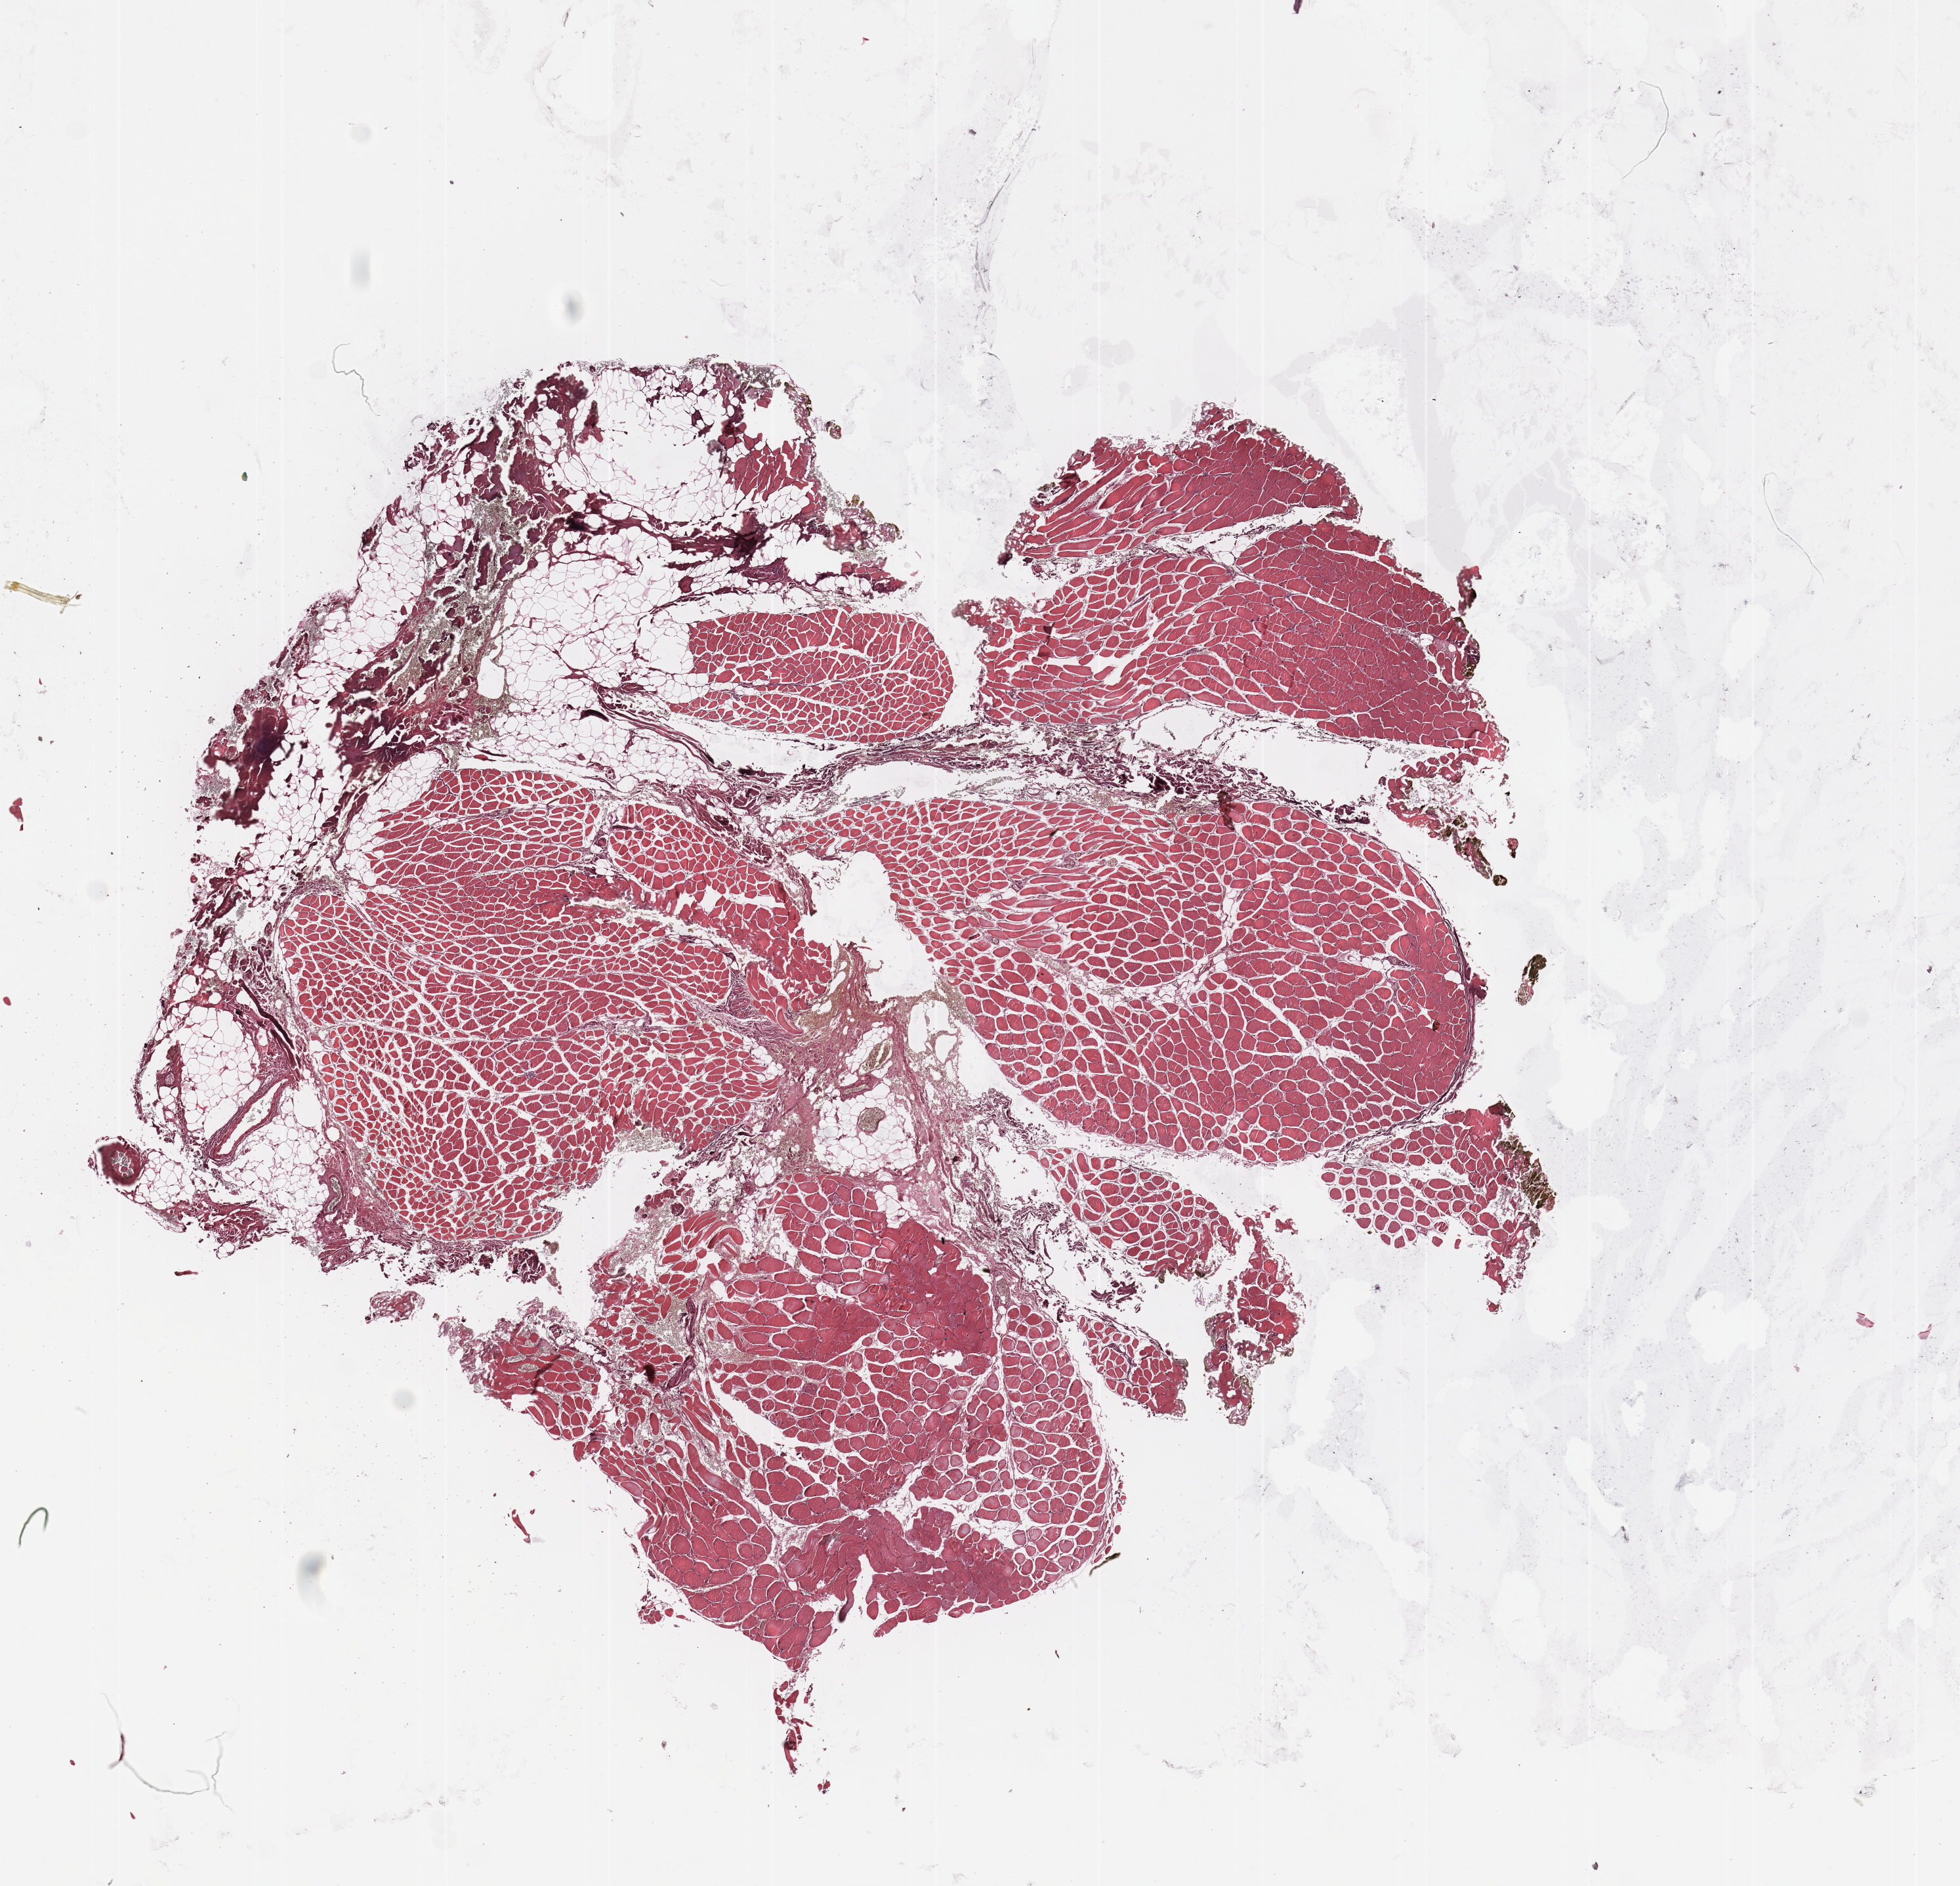
Hematoxylin and eosin (H&E) stained whole-slide image, shown as a low-resolution overview of the whole scanned area (about 11.8 x 11.4 mm, from a 20x scan). Normal (non-tumour) tissue sample. 67-year-old female patient.
This section: normal (non-tumour) tissue from the same patient. Patient diagnosis (cohort enrolment): sarcoma (site not recorded at cohort level).